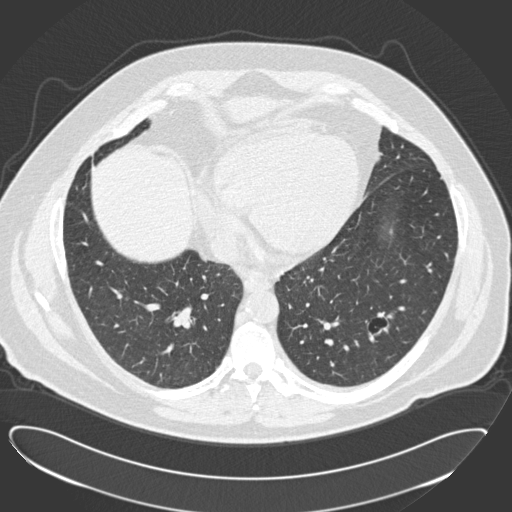
Chest CT (low-dose screening protocol), one axial image; baseline screening round; lung window (W 1500 / L -600 HU); 2 mm slice thickness; 120 kVp; slice 94 of 183 in the series. Male participant, aged 57 years at enrolment. Current smoker at enrolment.
• Expert reader's lesion annotation, box from (x=357, y=302) to (x=410, y=354) px.
• The screening reader recorded 2 non-calcified nodules or masses ≥4 mm on this exam; which of them this box marks is not recorded.
• Official screen result: positive, change unspecified: nodule(s) >= 4 mm or enlarging nodule(s), mass(es), or other non-specific abnormalities suspicious for lung cancer.
• Participant outcome: lung cancer diagnosed 791 days after this screen — squamous cell carcinoma, NOS, left lower lobe, moderately differentiated (G2), stage IA (AJCC 6th edition), 22 mm at pathology.